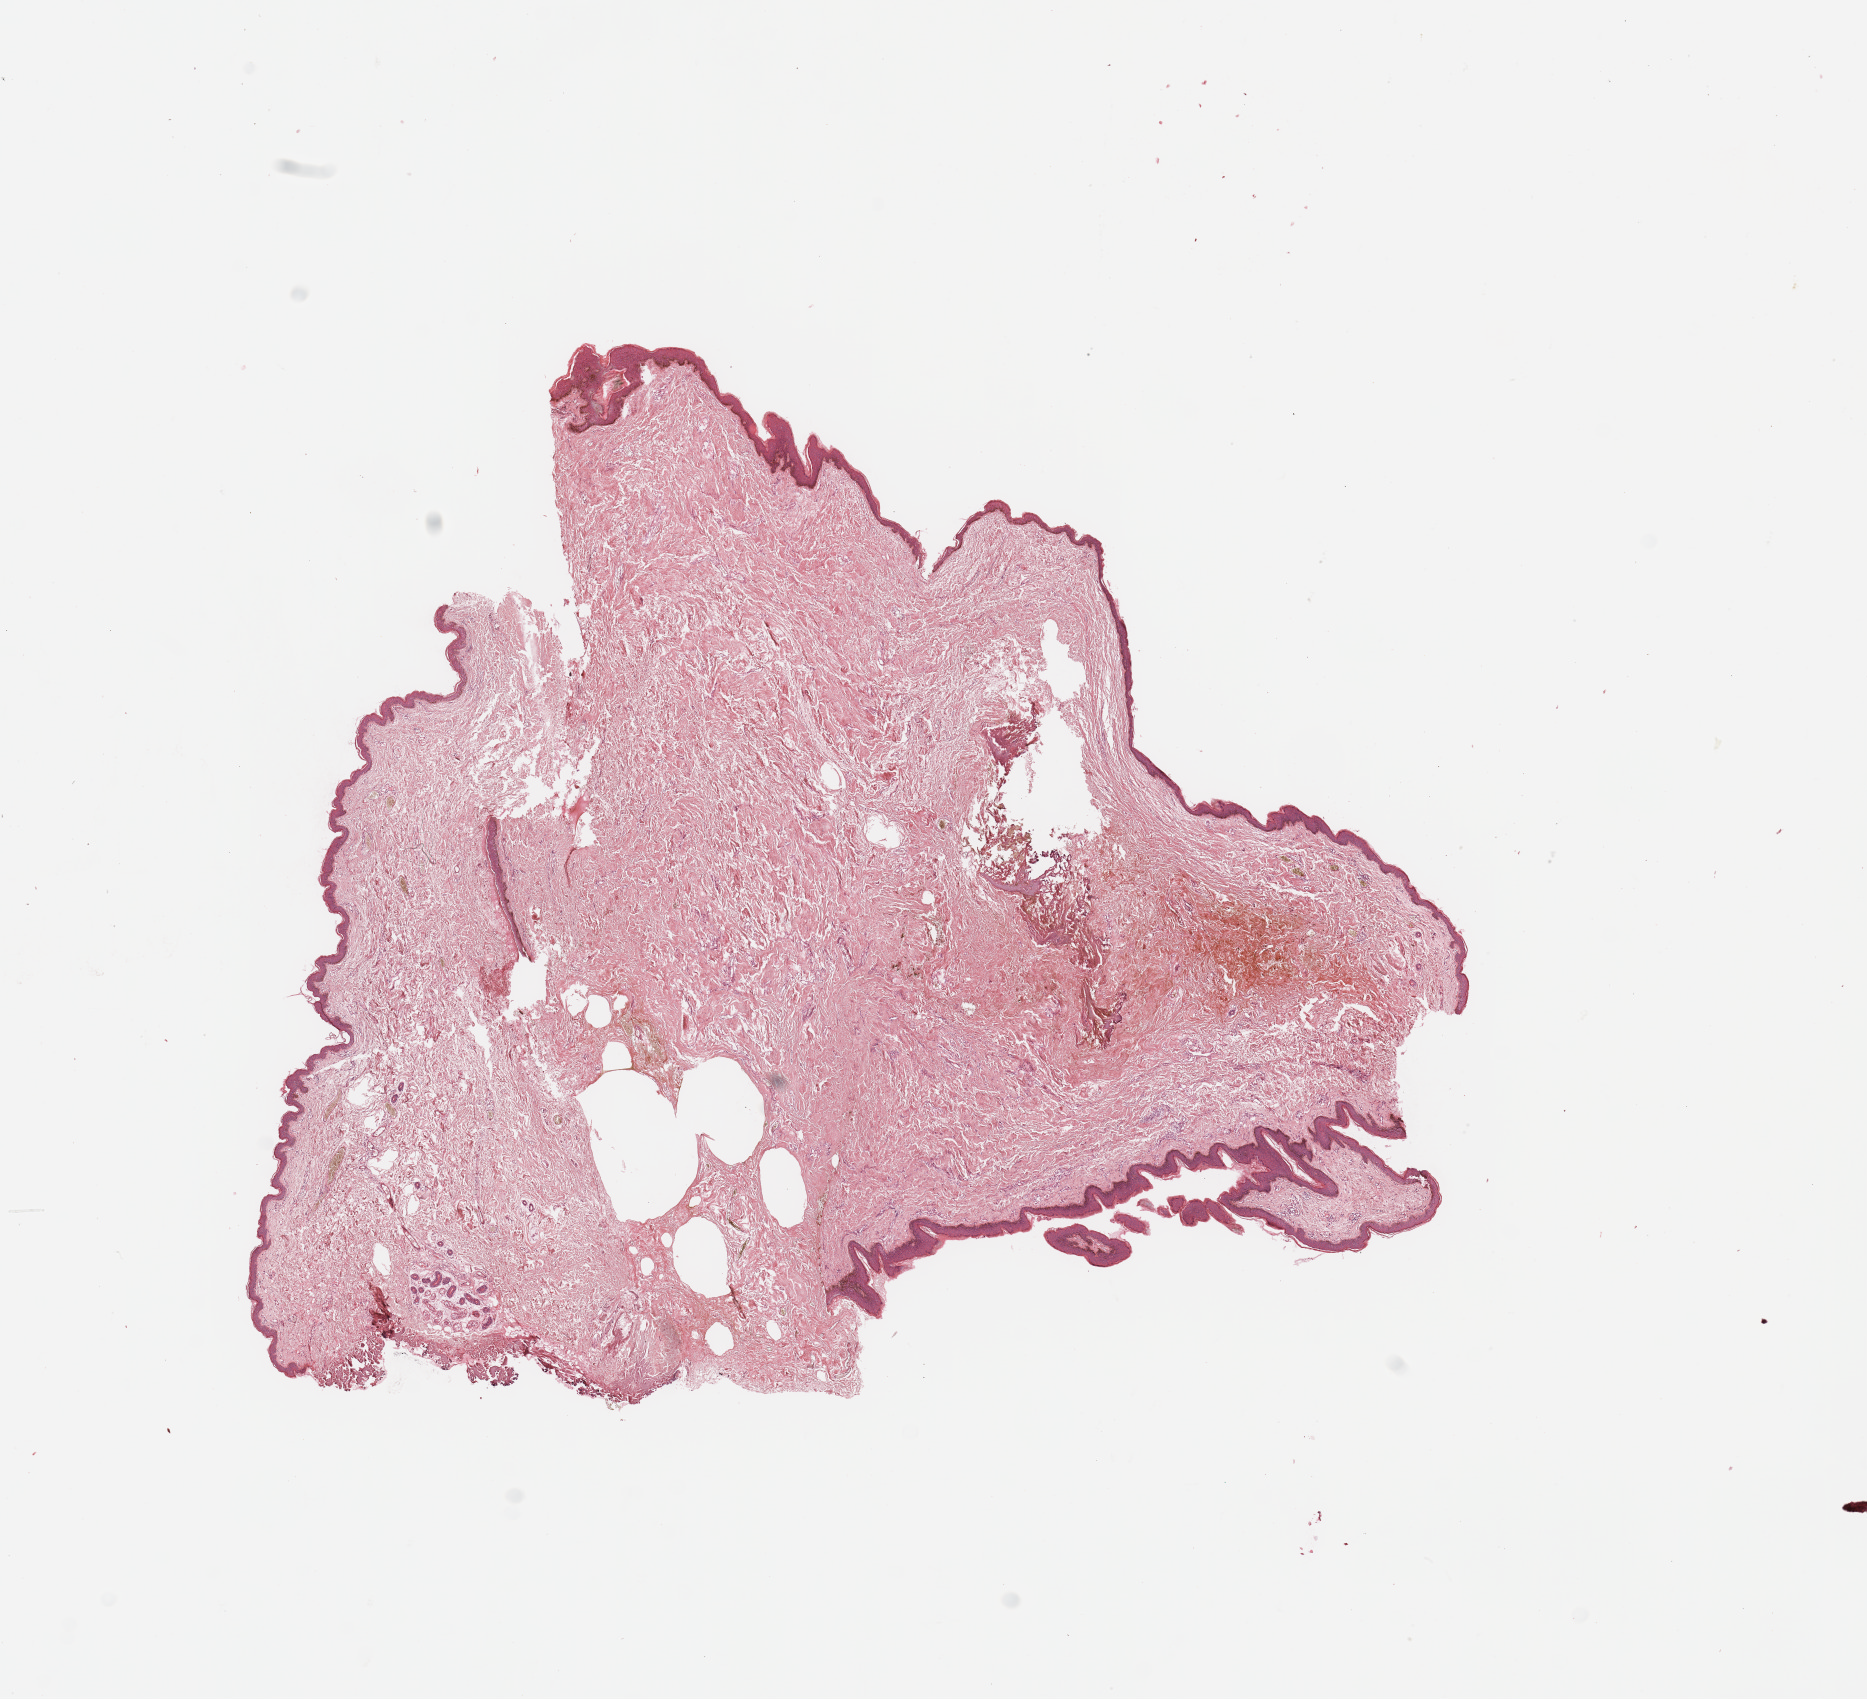
H&E-stained whole-slide image, a low-resolution overview of the entire scanned area, about 14.8 x 13.4 mm, normal (non-tumour) tissue sample. 66-year-old male patient.
This section: normal (non-tumour) tissue from the same patient. Patient diagnosis (cohort enrolment): sarcoma (site not recorded at cohort level).